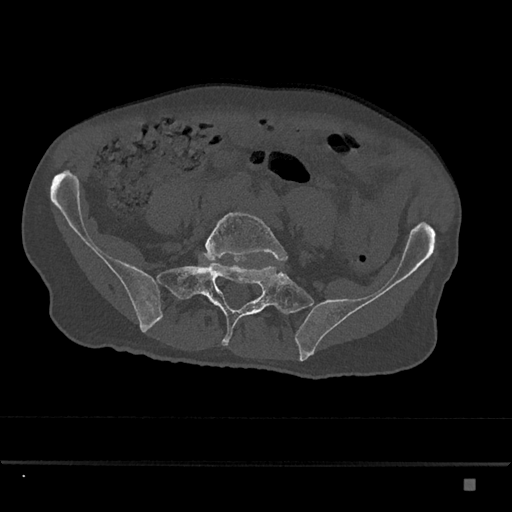
CT including the spine, one axial slice. Slice 244 of 797 in the series (ordered by position). Reconstruction kernel Br40s/3. 120 kVp. Bone window (W 1800 / L 400 HU). 0.5 mm slice thickness. 512 × 512 image matrix, field of view 390 × 390 mm. Patient: male, 72 years. Case-level facts recorded for this patient, not image findings: primary cancer: prostate.
Structures marked on this image (semi-automatic segmentation, software-assisted and operator-edited):
- L5 vertebra: bounding box <205,212,288,269> (left, top, right, bottom; pixels)